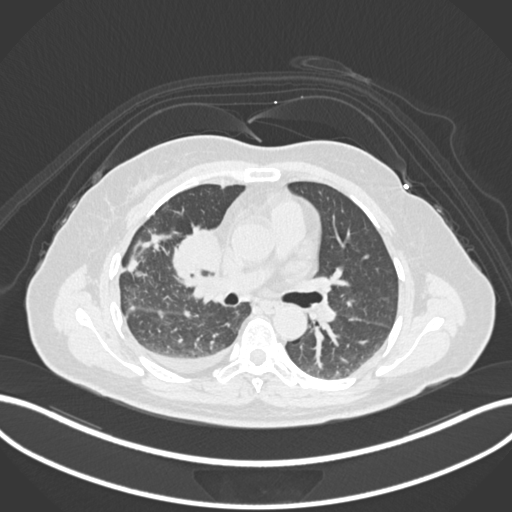
Chest CT, one axial slice; slice 79 of 172 in the series (ordered by position); lung window (W 1500 / L -600 HU); 512 × 512 image matrix, field of view 400 × 400 mm. Female patient, age 52 years. From the clinical record (not read from this slice): clinical TNM (as recorded): T3 N1 M1.
Annotated regions visible in this slice (rectangle marked by the reading radiologist):
- lung tumour (recorded histology: adenocarcinoma): box from (x=170, y=224) to (x=223, y=279) px